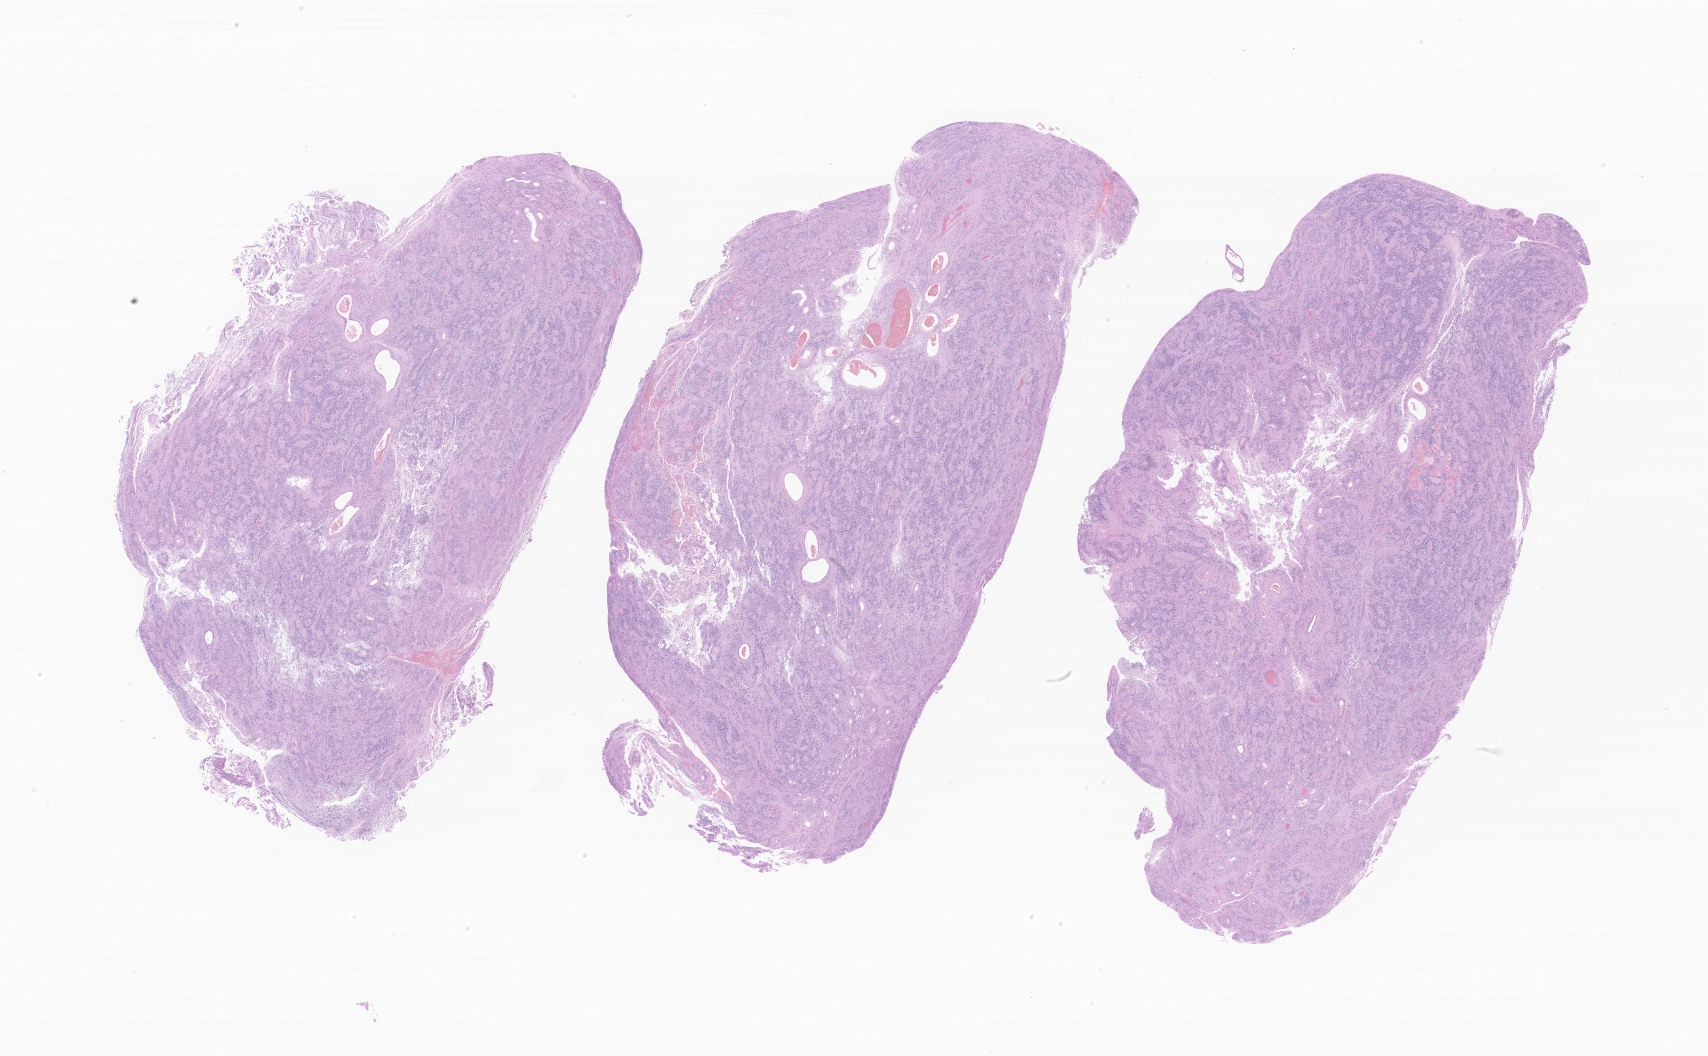
Haematoxylin and eosin whole-slide image of tumor tissue from the brain, a low-resolution overview of the entire scanned area, about 28.8 x 17.8 mm. FFPE section. Patient: female, age 277 months (23 years 1 month).
• recorded diagnosis: Ependymoma, NOS